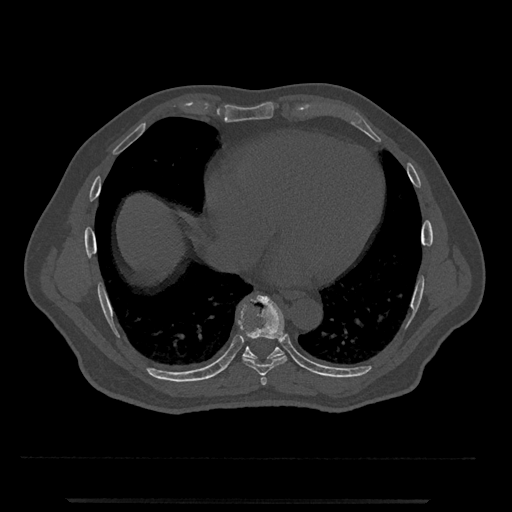
CT including the spine, one axial slice; slice 607 of 797 in the series (ordered by position); reconstruction kernel Br40s/3; bone window (W 1800 / L 400 HU); 512 × 512 image matrix, field of view 419 × 419 mm. Male patient, age 63 years. Case-level facts recorded for this patient, not image findings: primary cancer: prostate.
Annotated regions visible in this slice (semi-automatically segmented with operator editing):
- T7 vertebra: box from (x=260, y=375) to (x=267, y=385) px
- T8 vertebra: (x=238, y=295)–(x=287, y=376)
- T9 vertebra: (x=223, y=346)–(x=284, y=371)